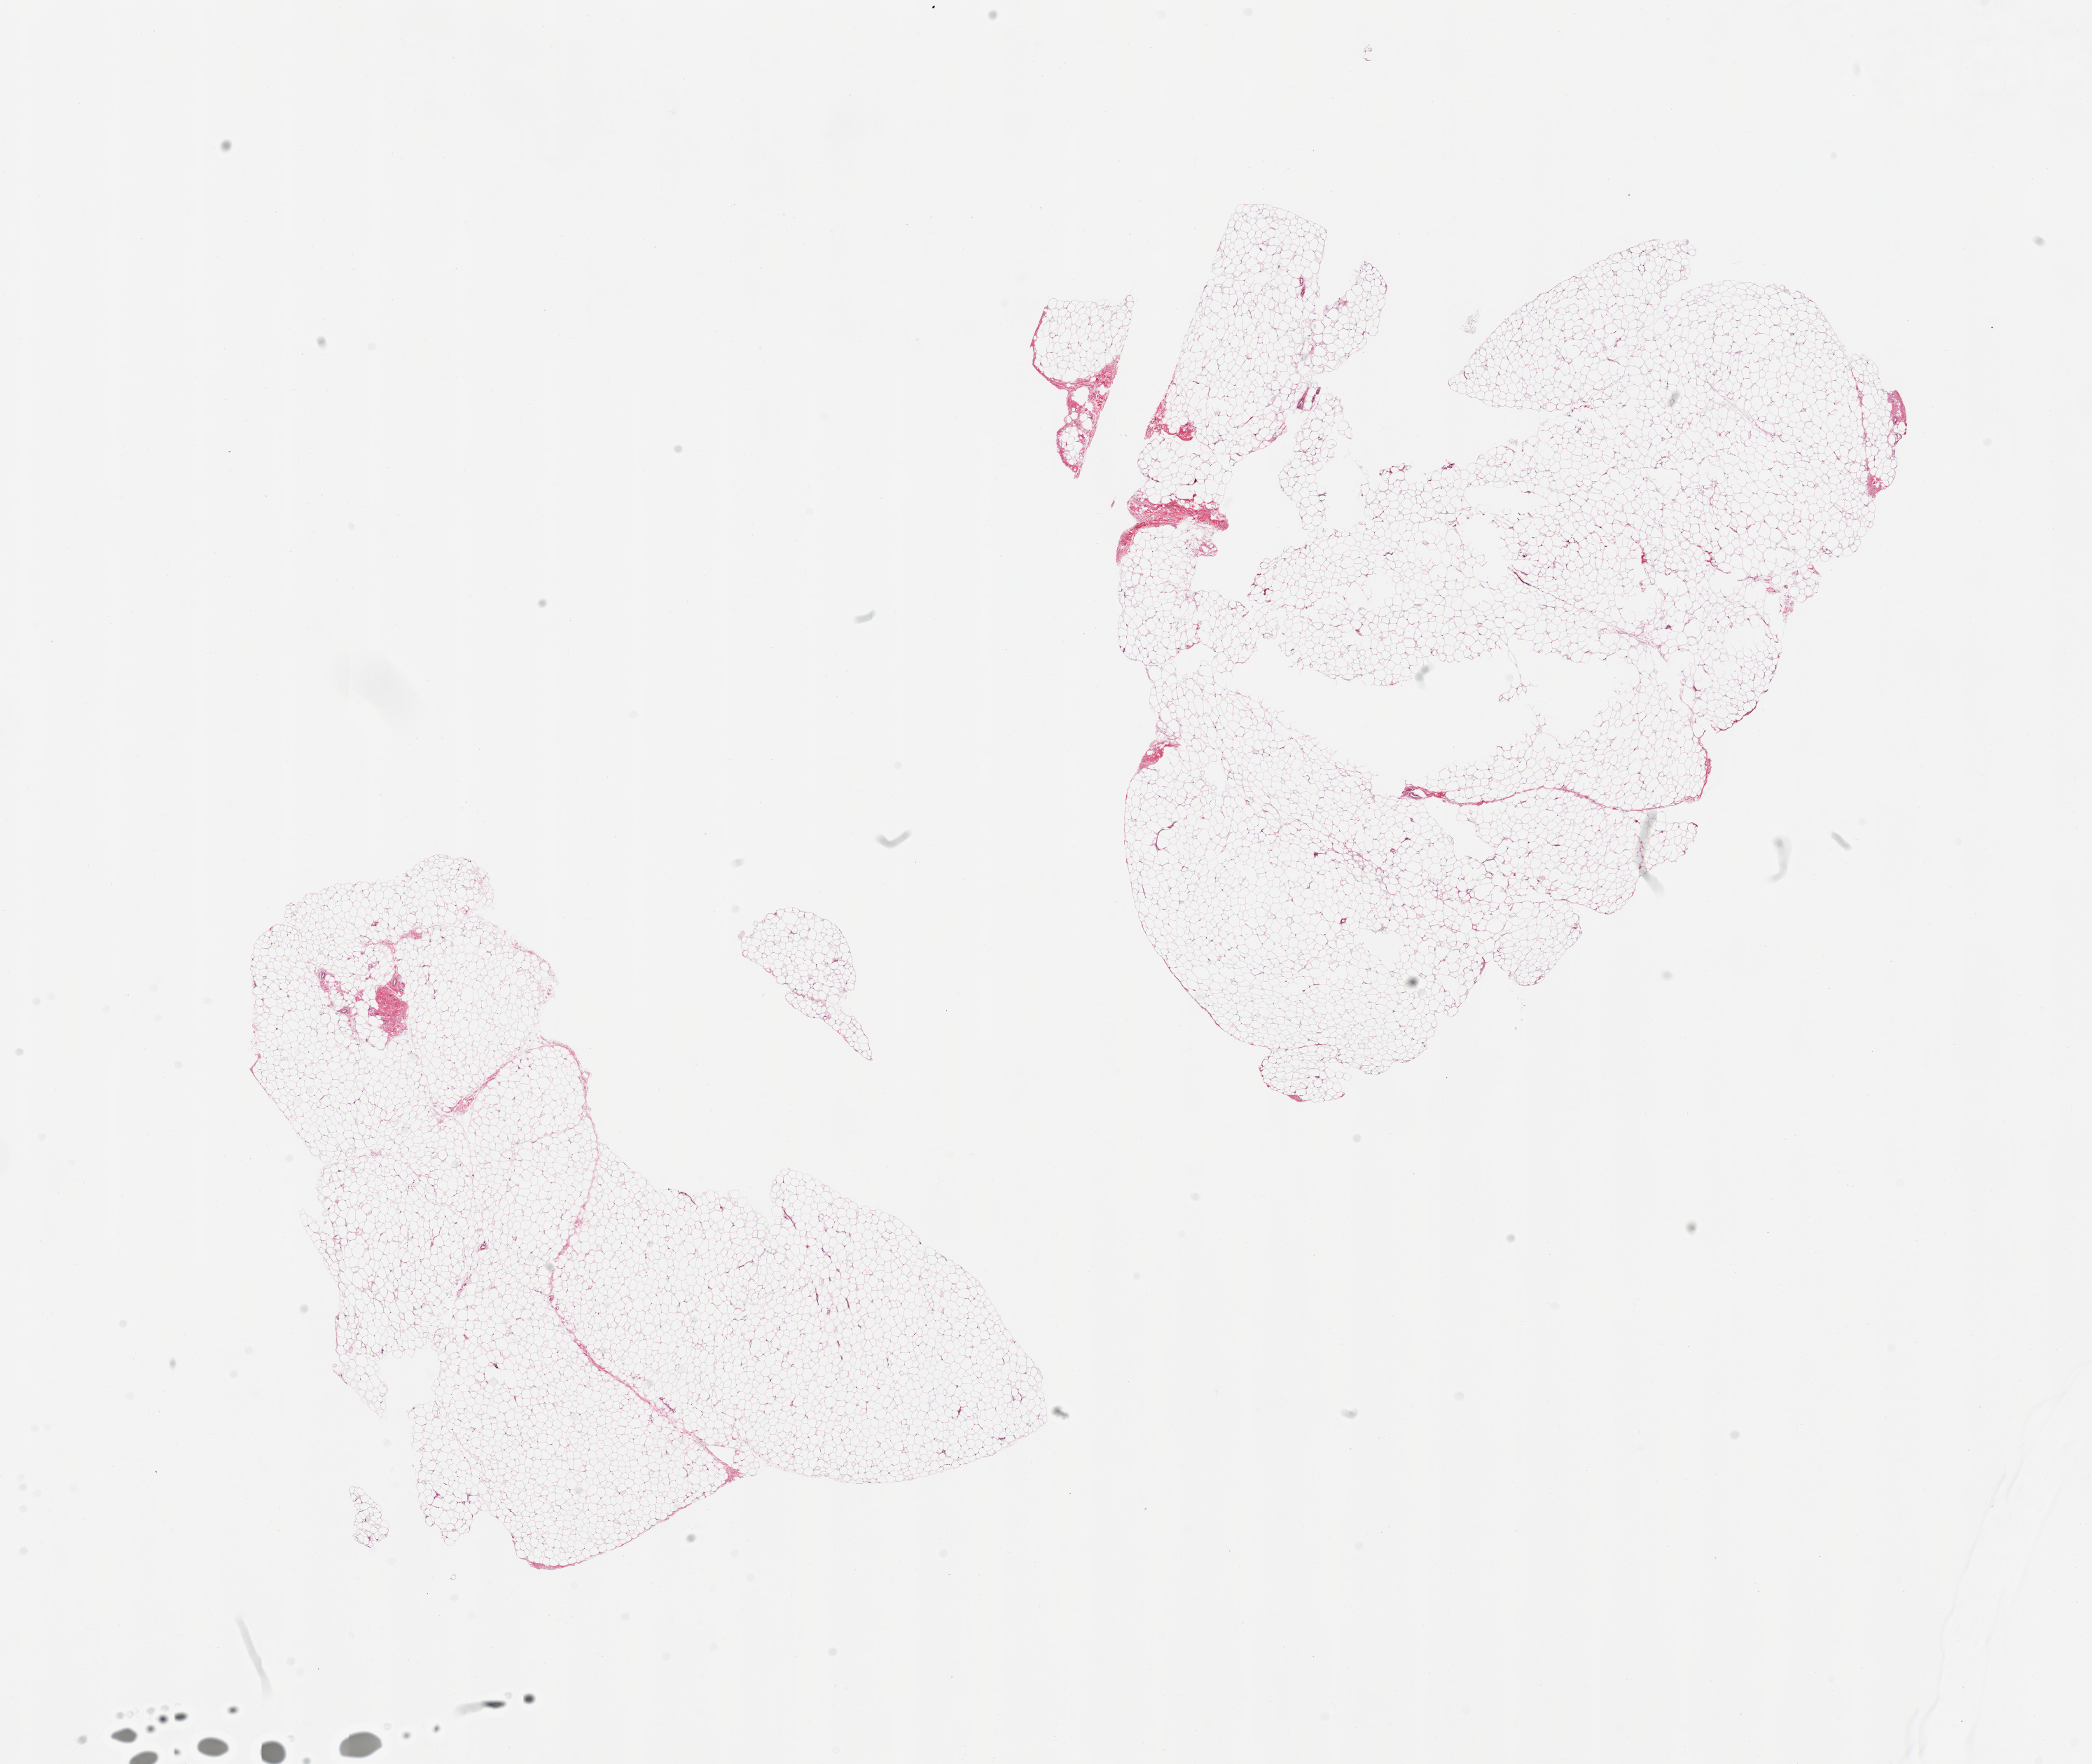
Hematoxylin and eosin (H&E) whole-slide image, brightfield — a low-resolution overview of the entire scanned area, about 23.6 x 19.9 mm. PAXgene-fixed, paraffin-embedded tissue. Target tissue: breast. Donor tissue sample. Donor: male.
* reviewer comment on this tissue sample: 2 pieces; adipose tissue only